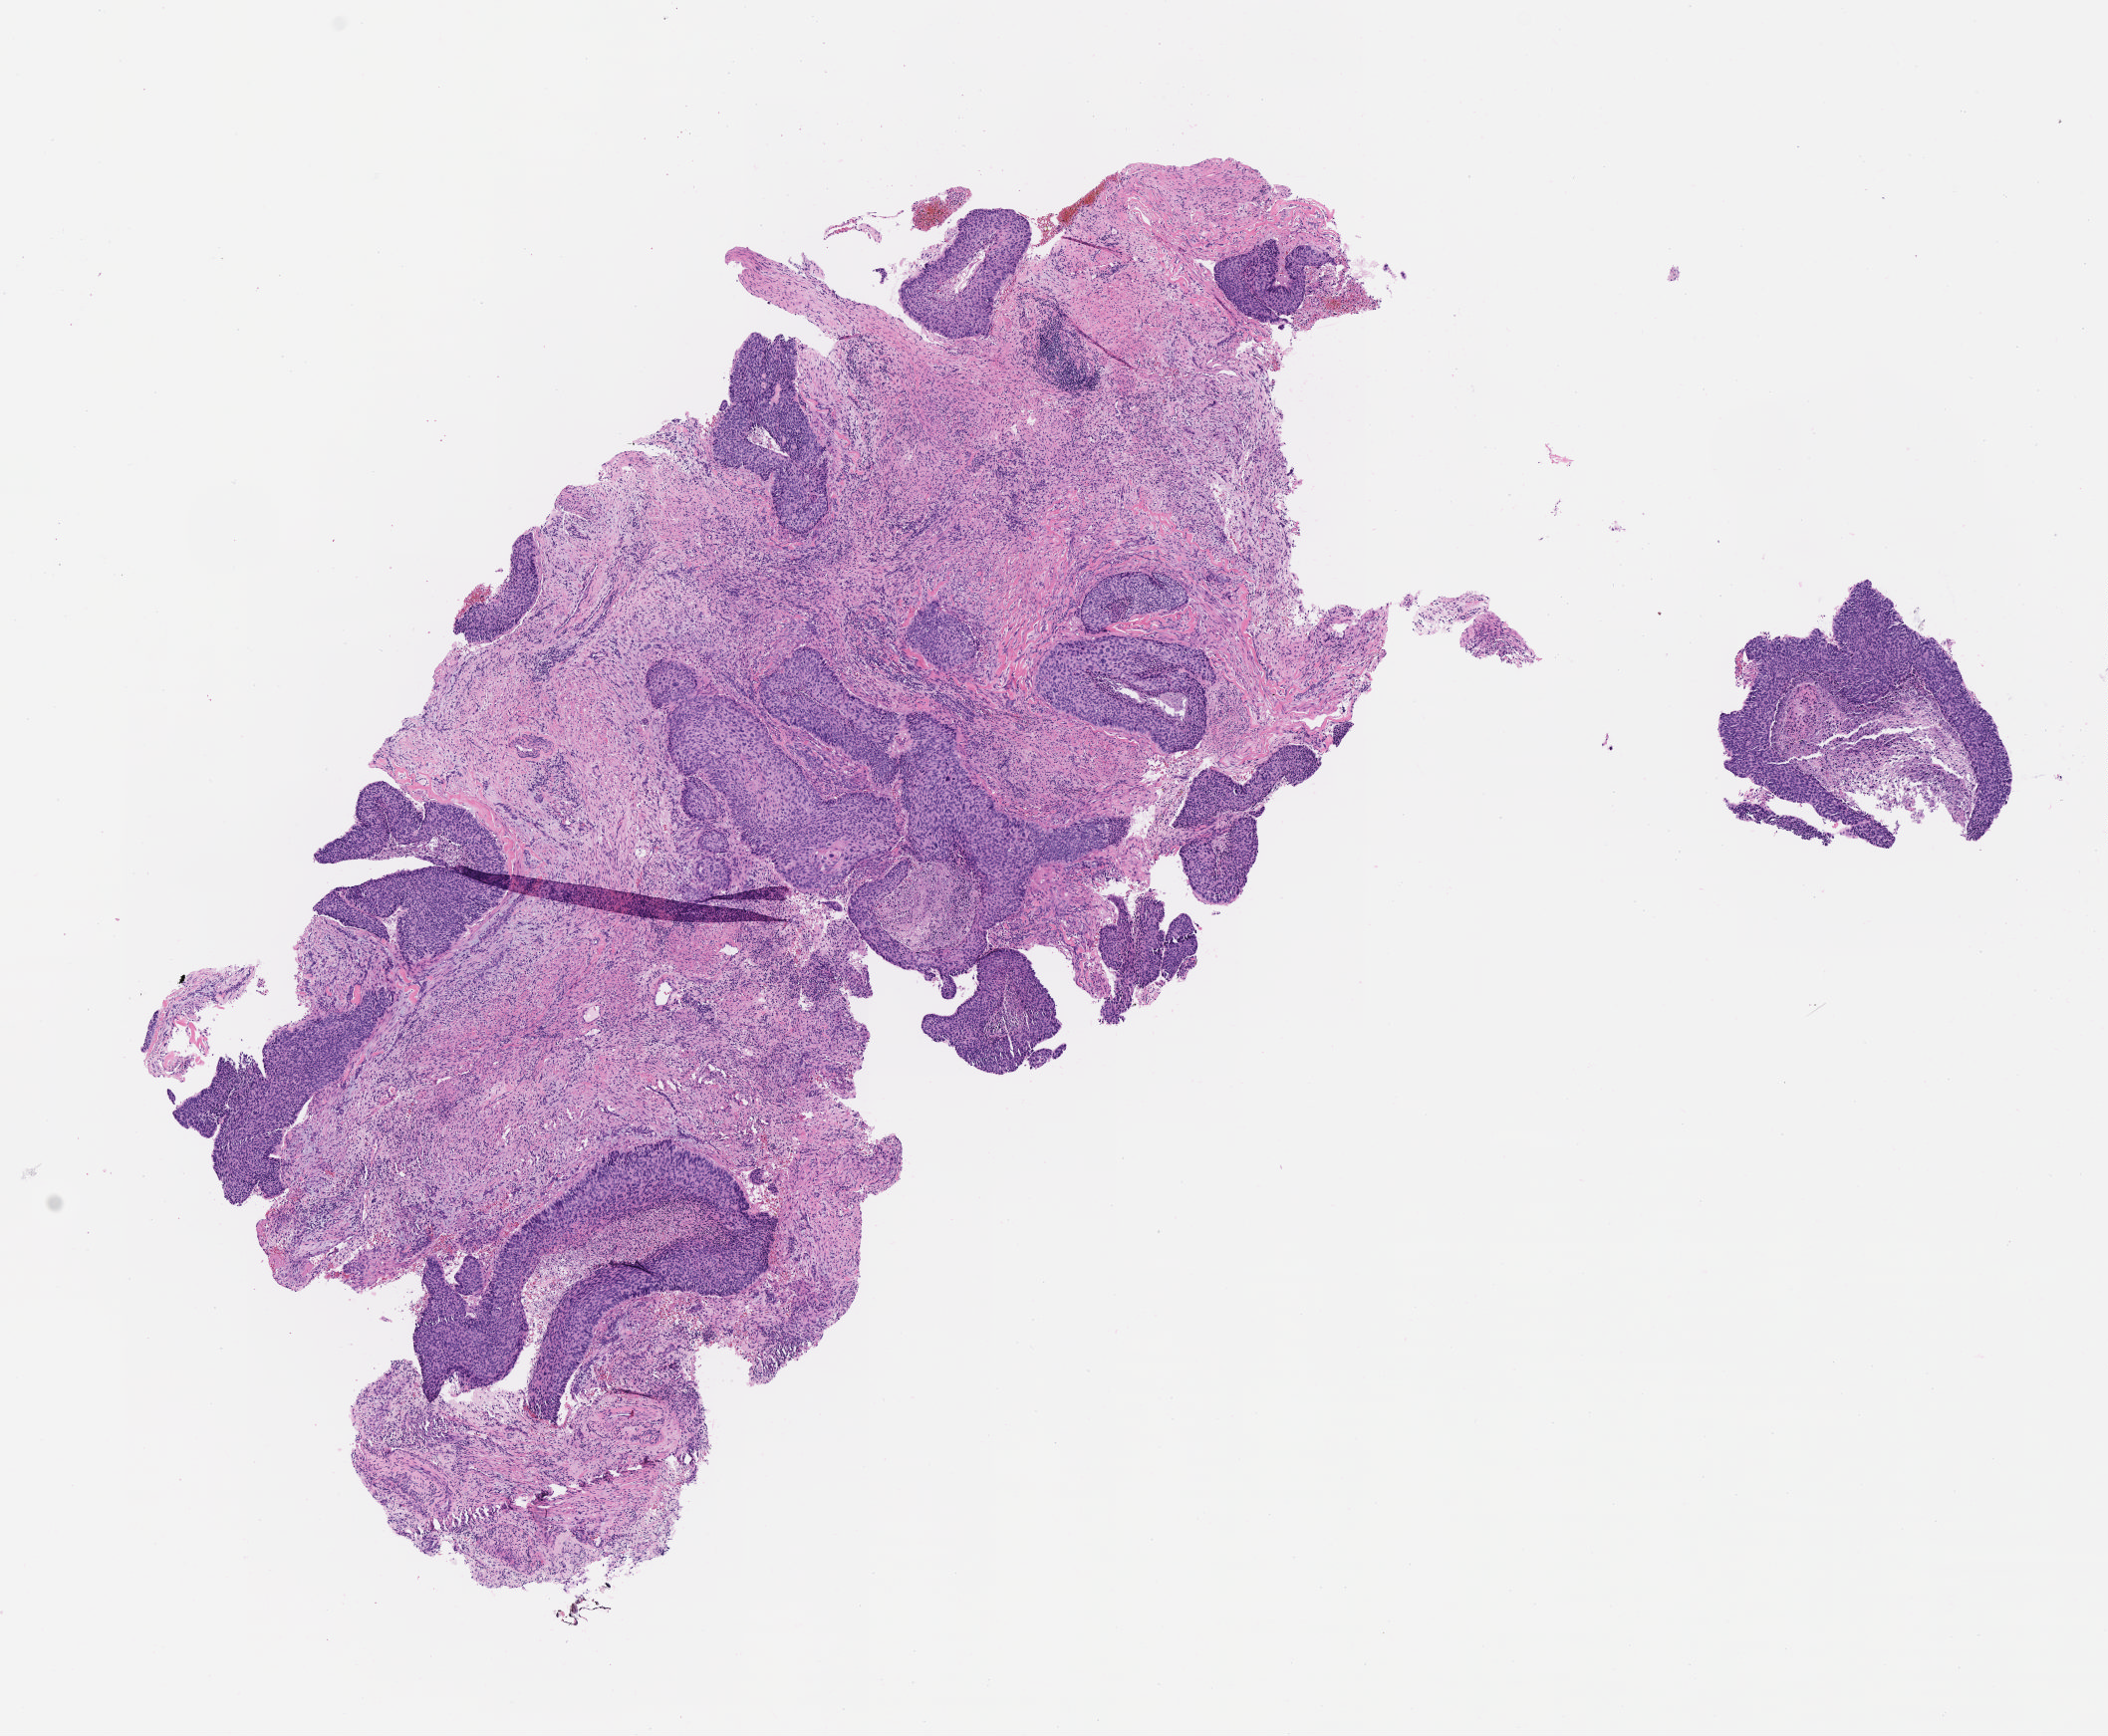
Hematoxylin and eosin (H&E) whole-slide image, a low-resolution overview of the entire scanned area, about 8.6 x 7.0 mm. Tumor tissue. Anatomic site: cervix. Female patient, age 54 years.
* diagnosis: Squamous cell carcinoma, large cell, nonkeratinizing, NOS